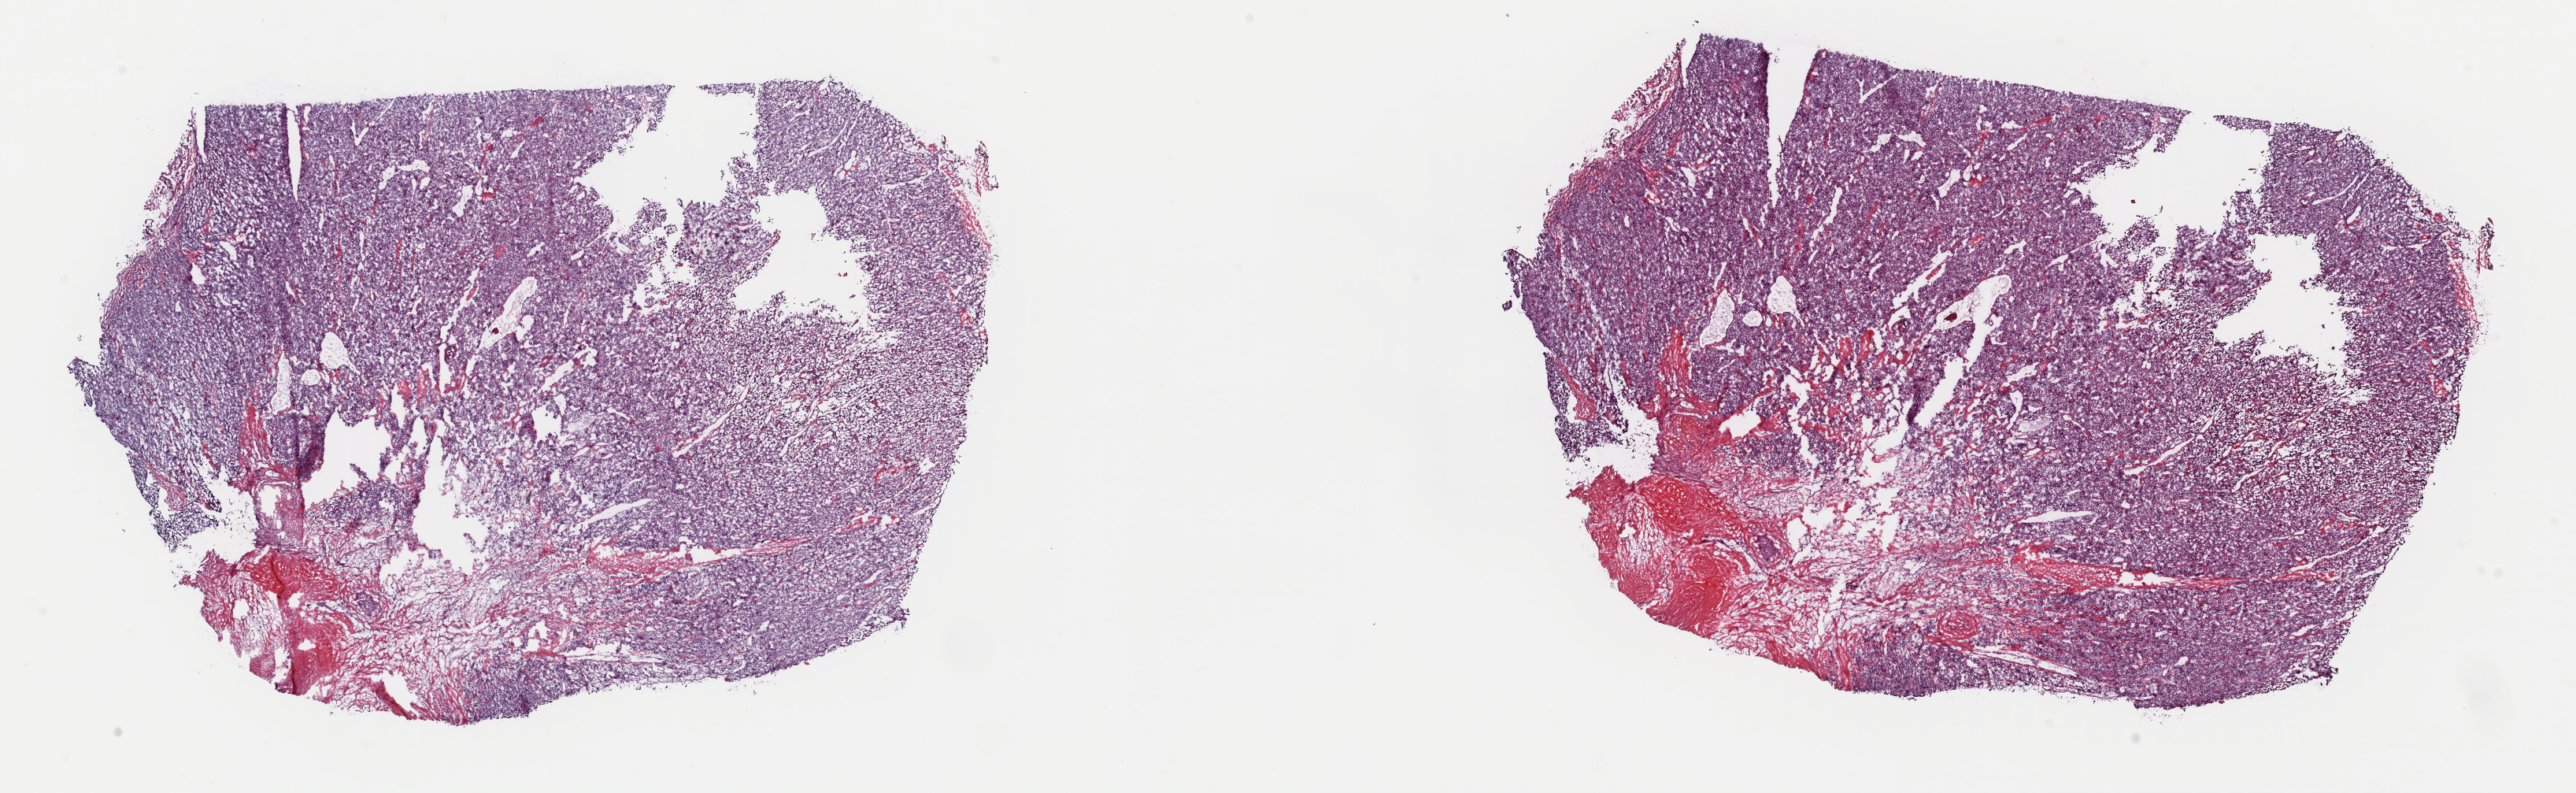
Whole-slide histology image, H&E-stained — a low-resolution overview of the entire scanned area, about 25.8 x 8.0 mm (from a 40x scan). Frozen section from the top of the tissue portion. Primary tumour sample. Male patient; age at initial diagnosis 46 years. Pathologist review of this section (percent, as recorded): tumour cells 80%, tumour nuclei 80%.
Histologic diagnosis: Extra-adrenal paraganglioma, malignant.